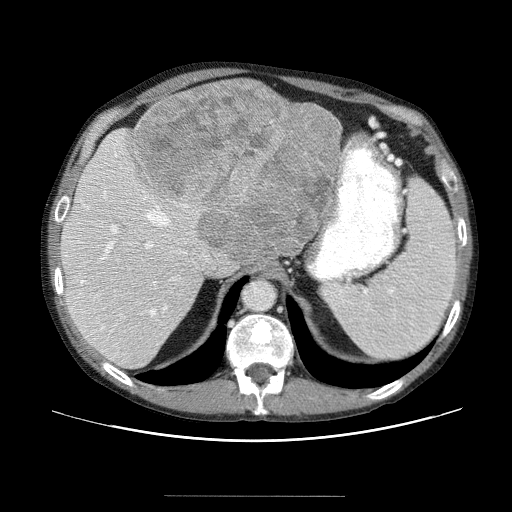
Contrast-enhanced abdominal CT (liver protocol), one axial slice. Position 38 of 69 along the scan axis. 120 kVp. Soft-tissue window (W 400 / L 40 HU). 2.5 mm slice thickness. 512 × 512 image matrix, field of view 380 × 380 mm. From the clinical record (not read from this slice): diagnosis: hepatocellular carcinoma (patient treated with transarterial chemoembolisation; whether this scan precedes or follows treatment is not stated here); TNM stage (as recorded): Stage-IVB; Child-Pugh class: B; tumour differentiation: poorly differentiated.
Annotated regions visible in this slice (semi-automatically segmented with operator editing):
- abdominal aorta: bounding box [x1, y1, x2, y2] px = [243, 280, 274, 310]
- liver parenchyma outside the tumour (the mass and vessels are separate outlines, so this box may not span the whole liver): [61, 90, 324, 370]
- mass: [133, 79, 342, 259]
- liver vessels: [75, 152, 200, 351]